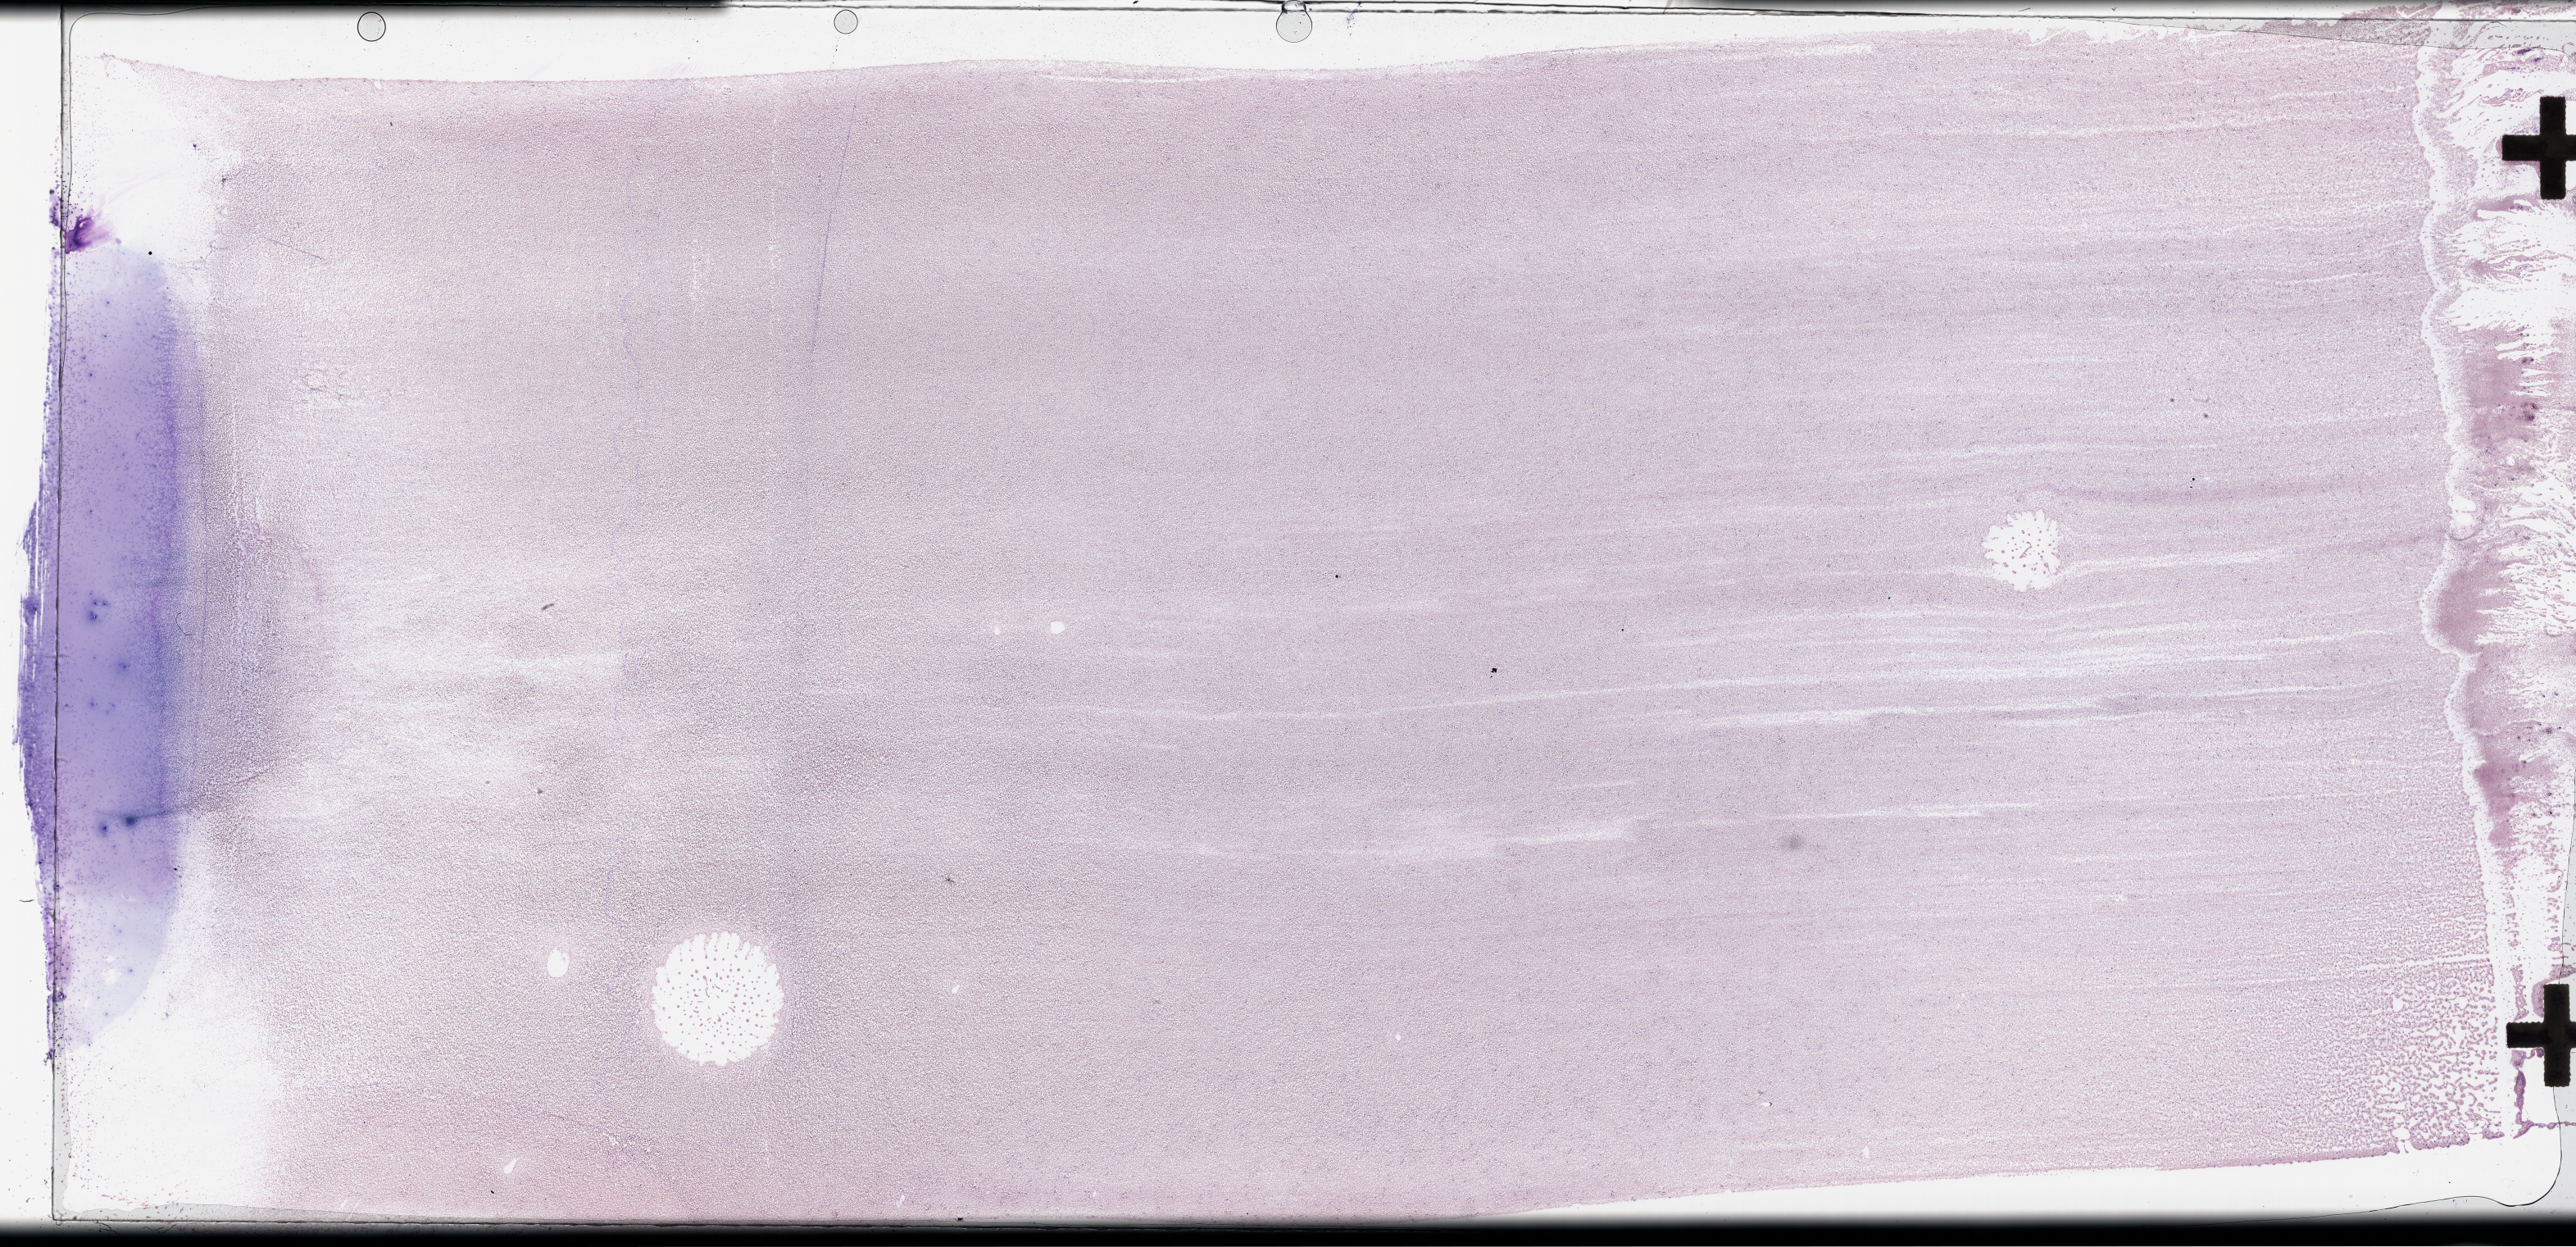
Digitized H&E tissue section (whole slide) — whole scanned area (about 50.8 x 24.6 mm, from a 40x scan) shown as a low-resolution overview. Peripheral blood (leukaemic) sample. Female, 57 y/o.
• FAB classification: M2
• diagnosis: Acute Myeloid Leukemia